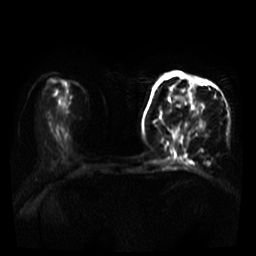
Breast MRI, one axial slice; slice 12 of 39 in the series (ordered by position); diffusion-weighted series; image 2 of 4 stored at this slice position (different b-values; order by instance number); 3 T; 5 mm slice thickness; 256 × 256 image matrix. Female patient.
Annotated regions visible in this slice (outlined manually by an expert reader):
- tumour on diffusion-weighted imaging: box from (x=167, y=76) to (x=205, y=145) px